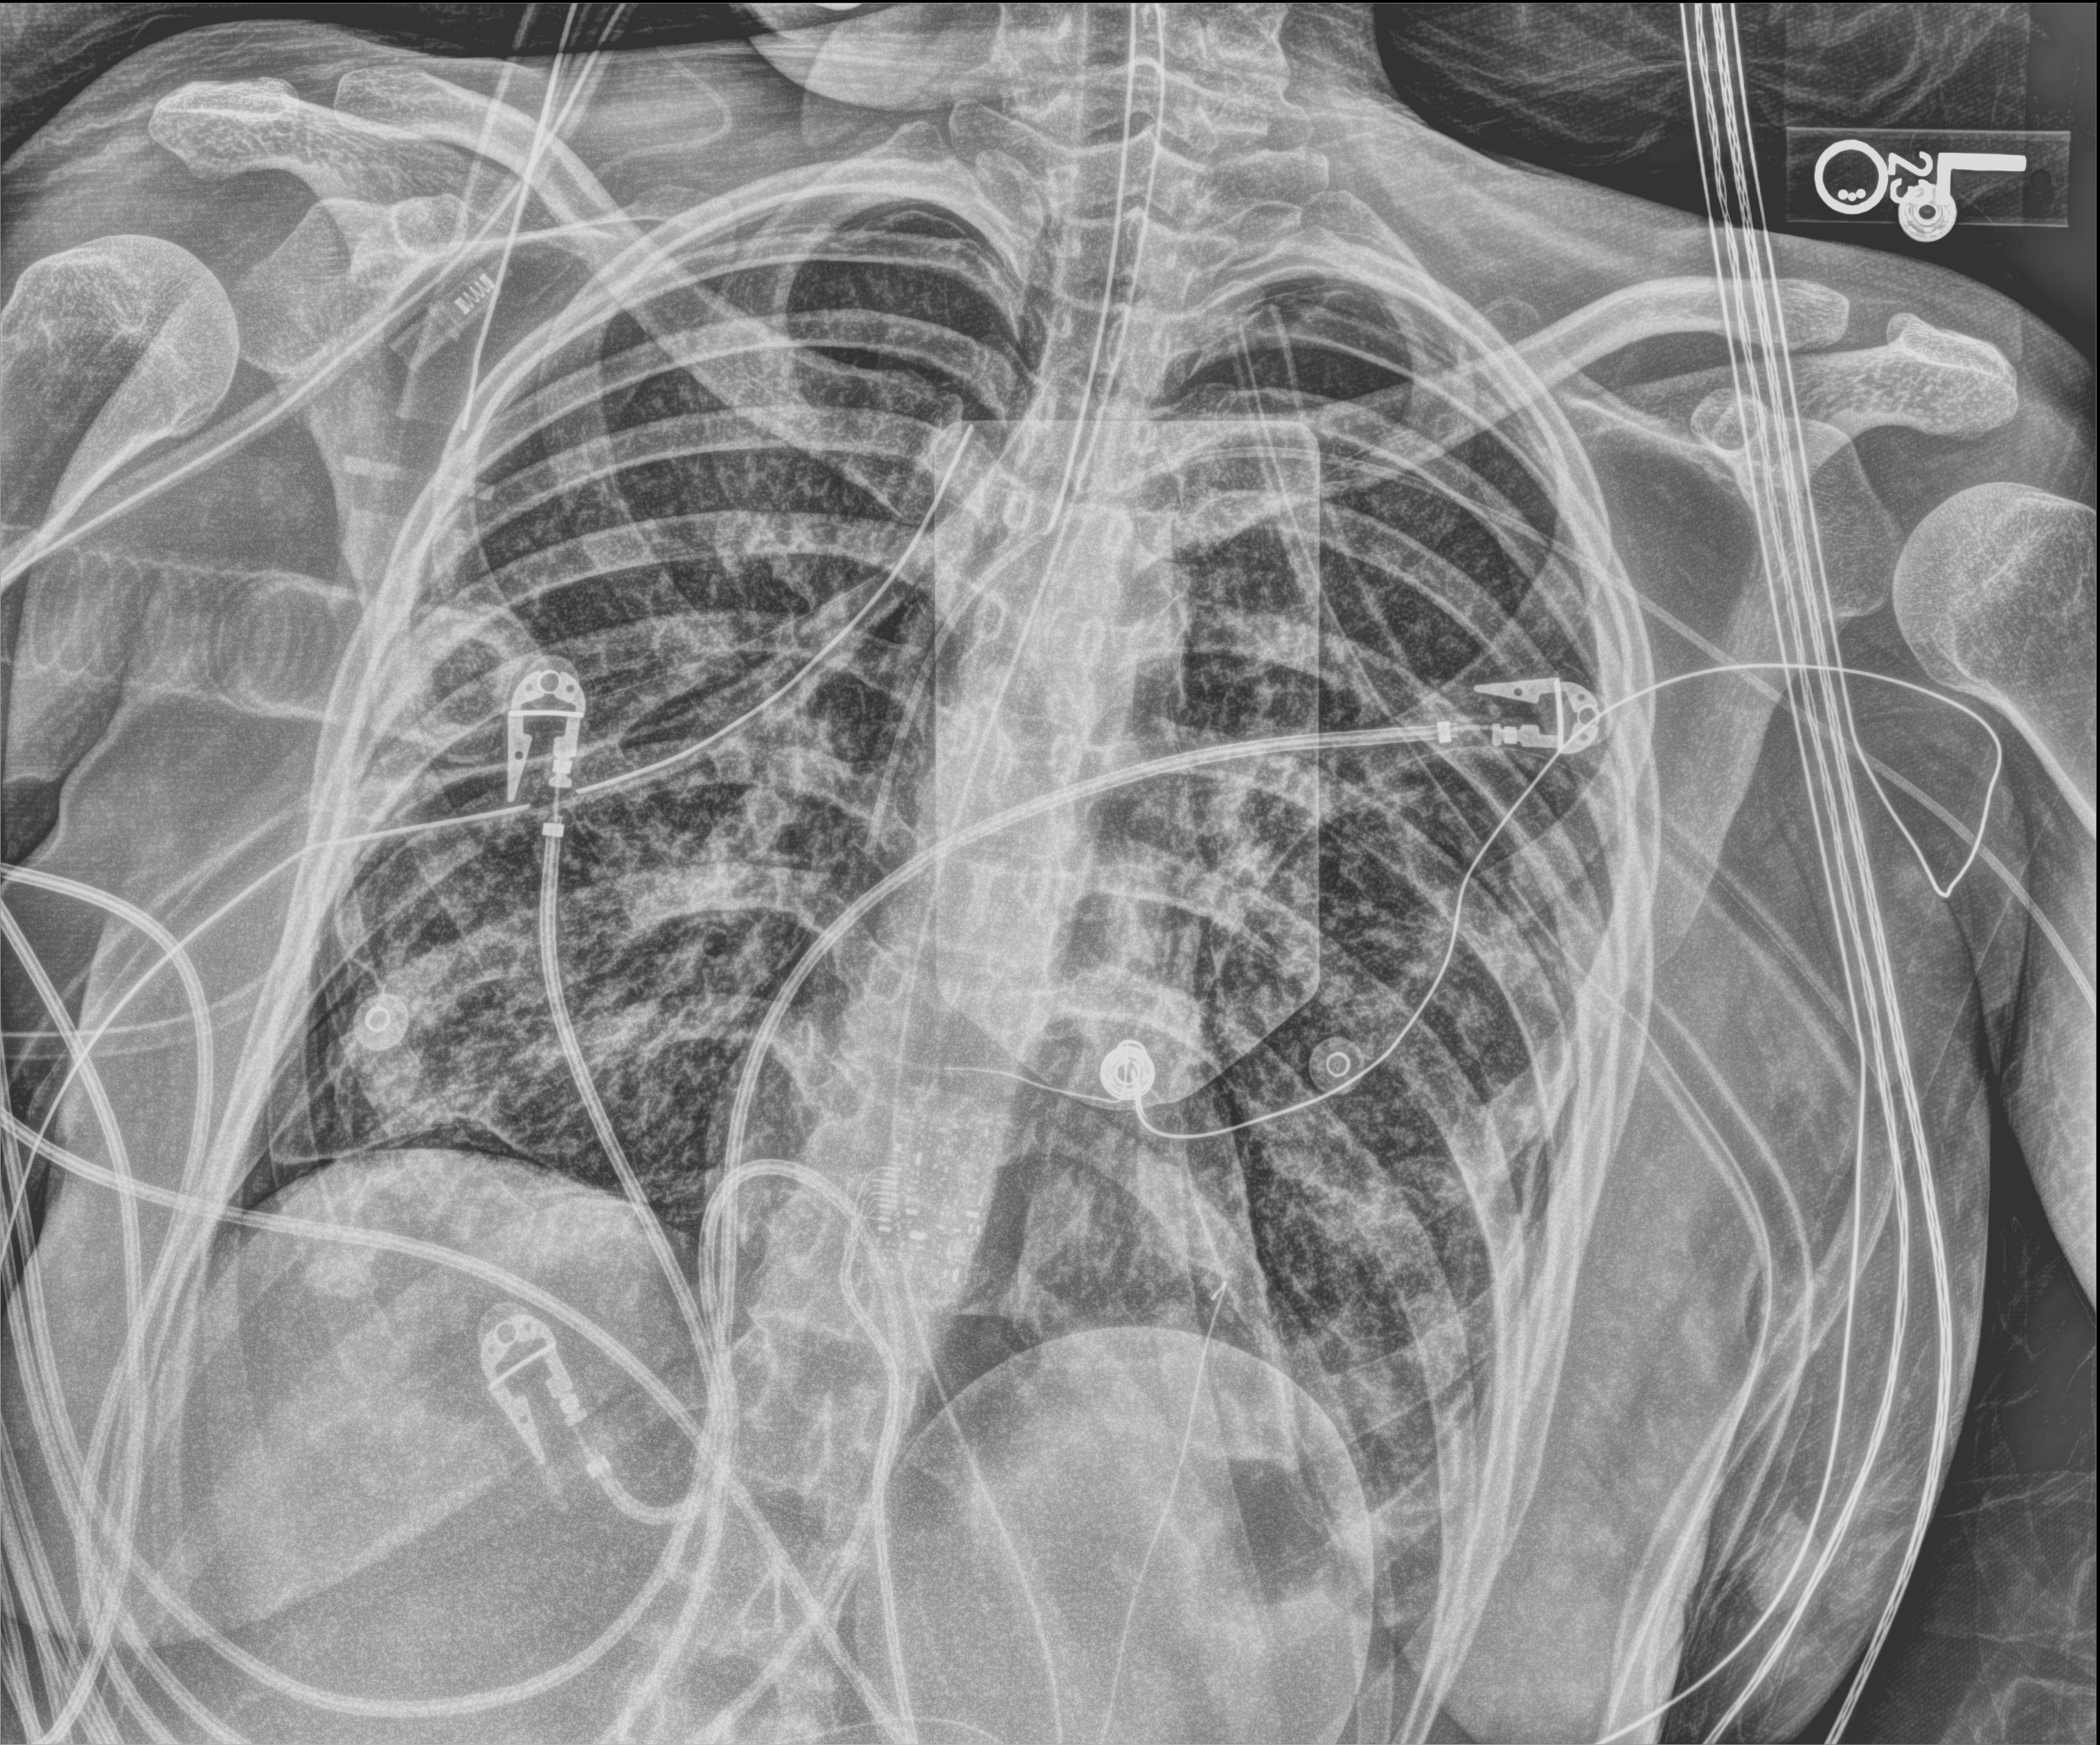
Portable chest radiograph. Patient hospitalised with COVID-19, aged 18–59 years.
Hospital-stay facts (about this admission, not read from this image; timing relative to this image not recorded):
- admitted to intensive care during this hospital stay: yes